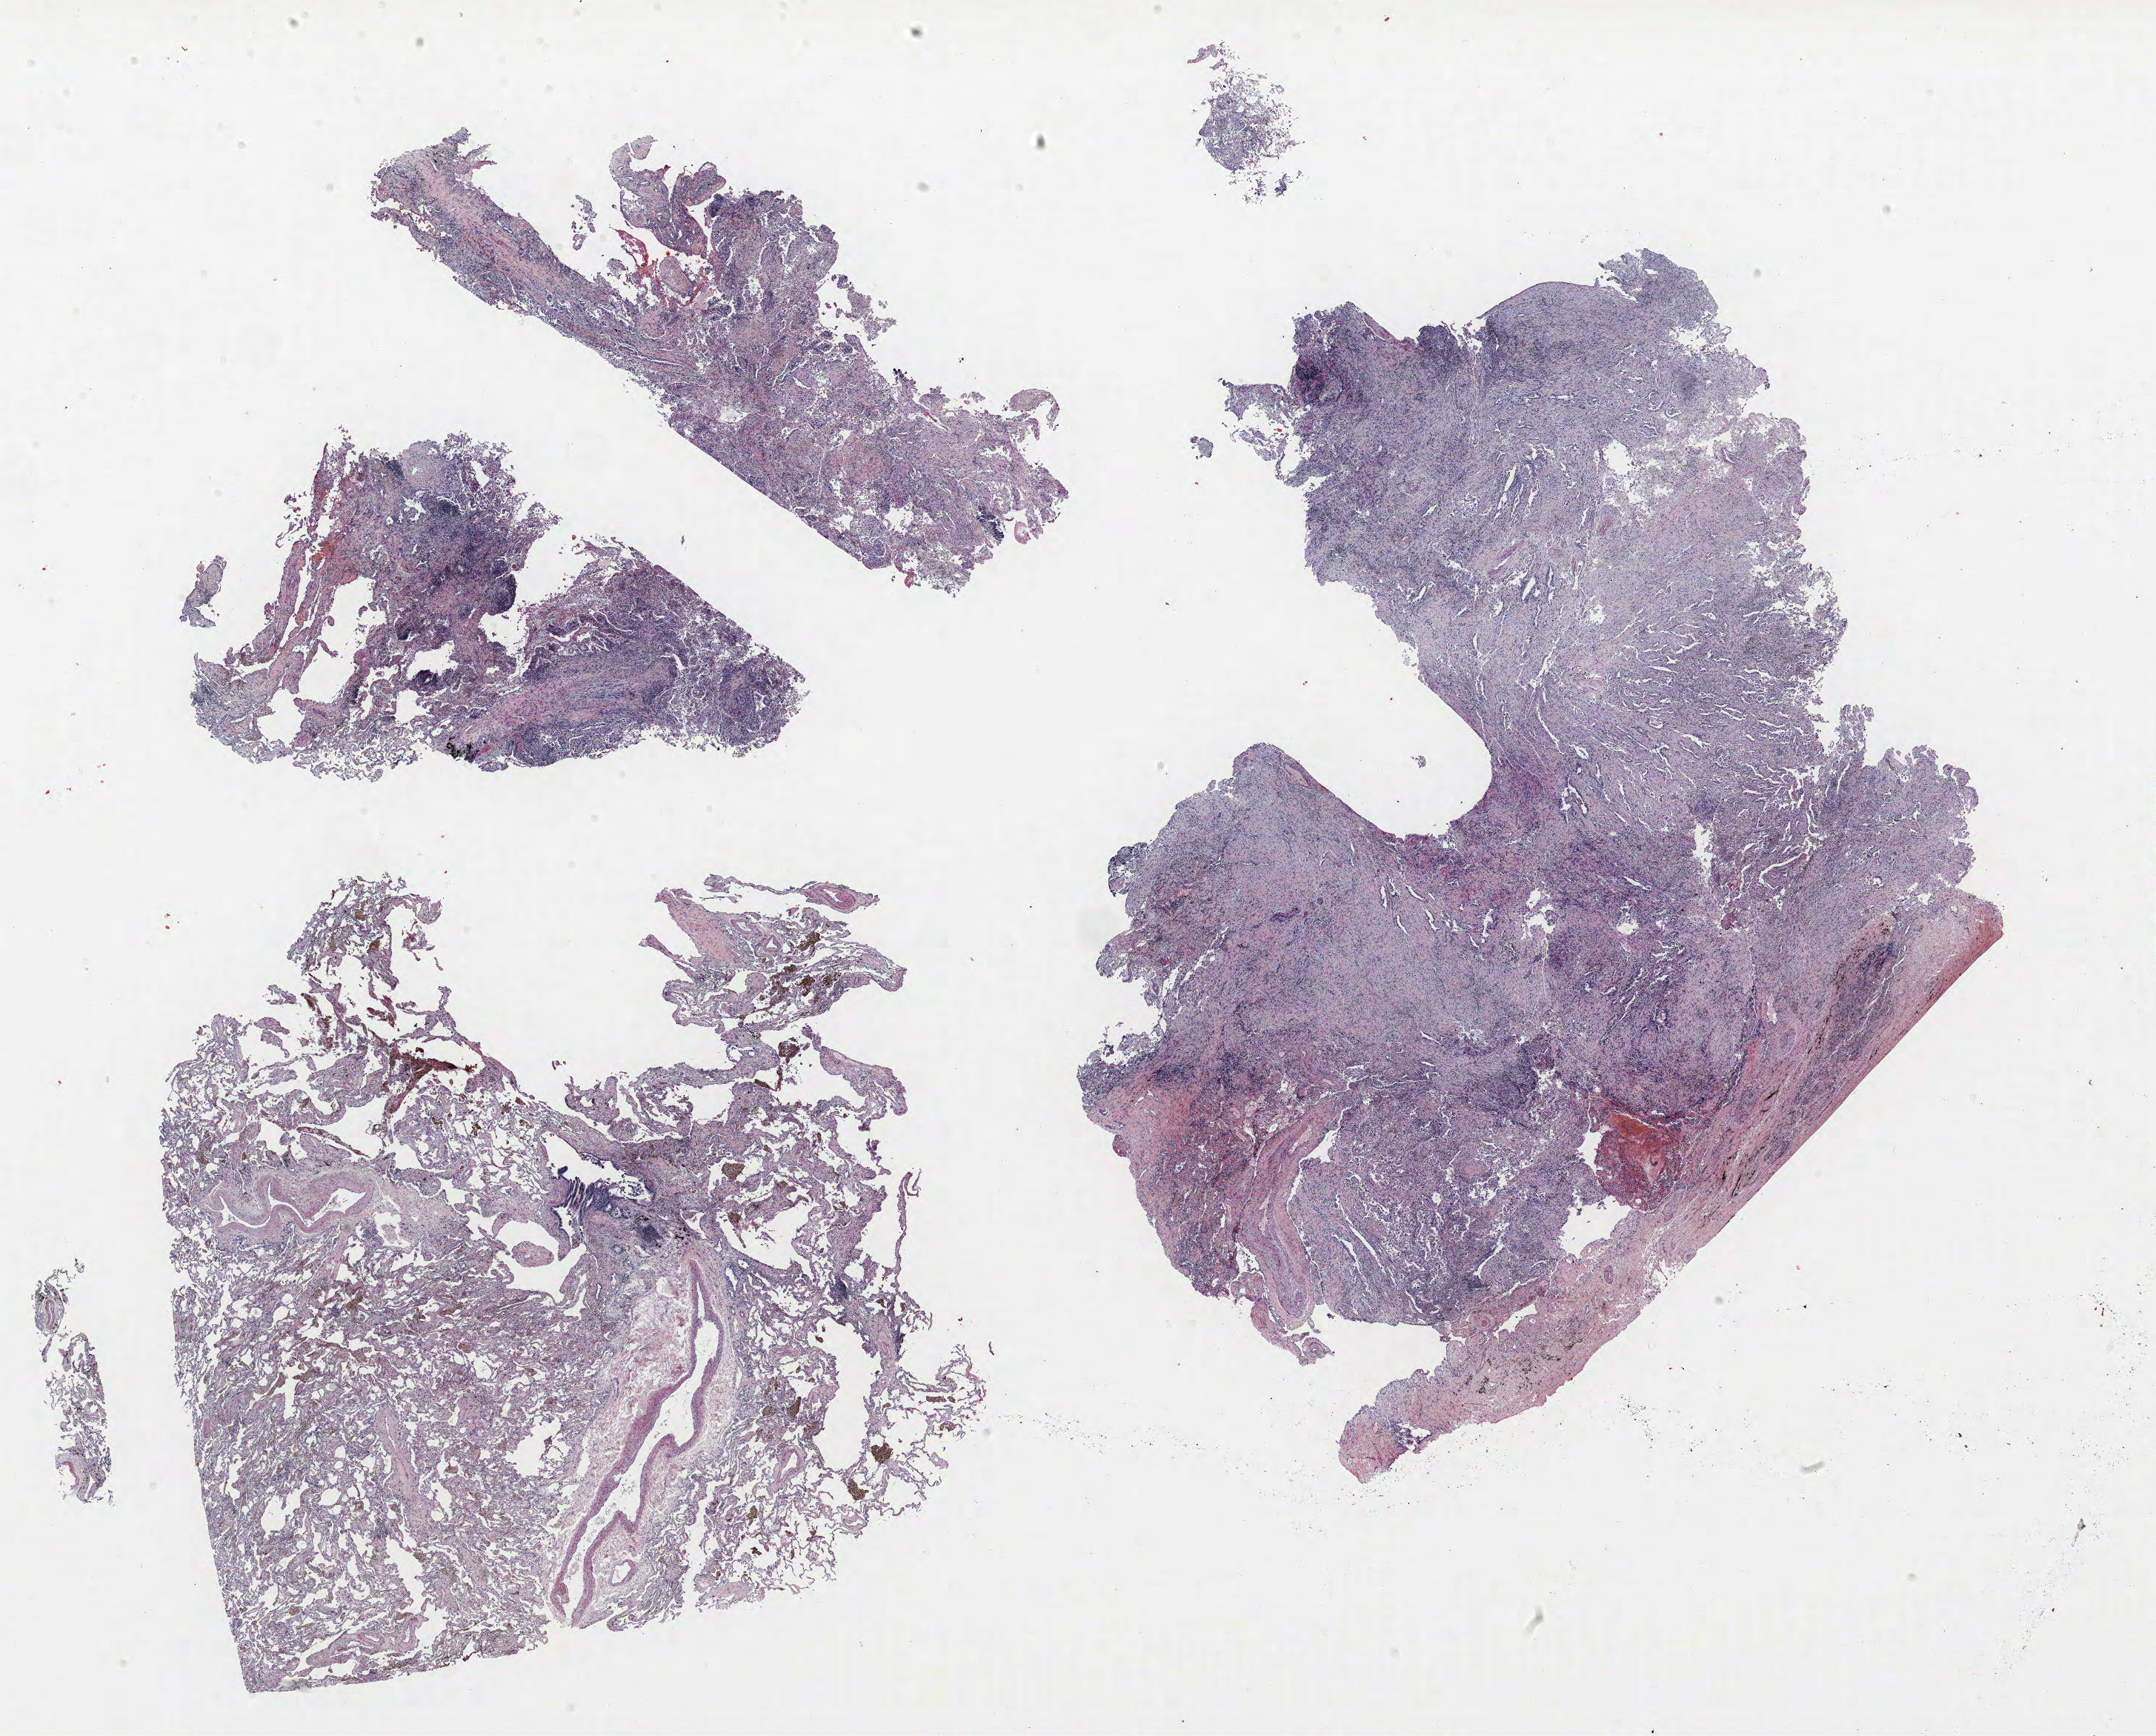
H&E-stained whole-slide image, low-resolution overview of the scanned area, about 23.3 x 18.7 mm (acquisition: 40x scan); formalin-fixed paraffin-embedded (FFPE) section; lung. Male patient, aged 68 at enrolment. Current smoker at enrolment.
Tumour size (pathology): 25 mm. Stage (AJCC 6th edition): IV. Primary tumour location (clinical record): left upper lobe. Participant's lung-cancer diagnosis: Adenocarcinoma, NOS (ICD-O-3 8140/3).